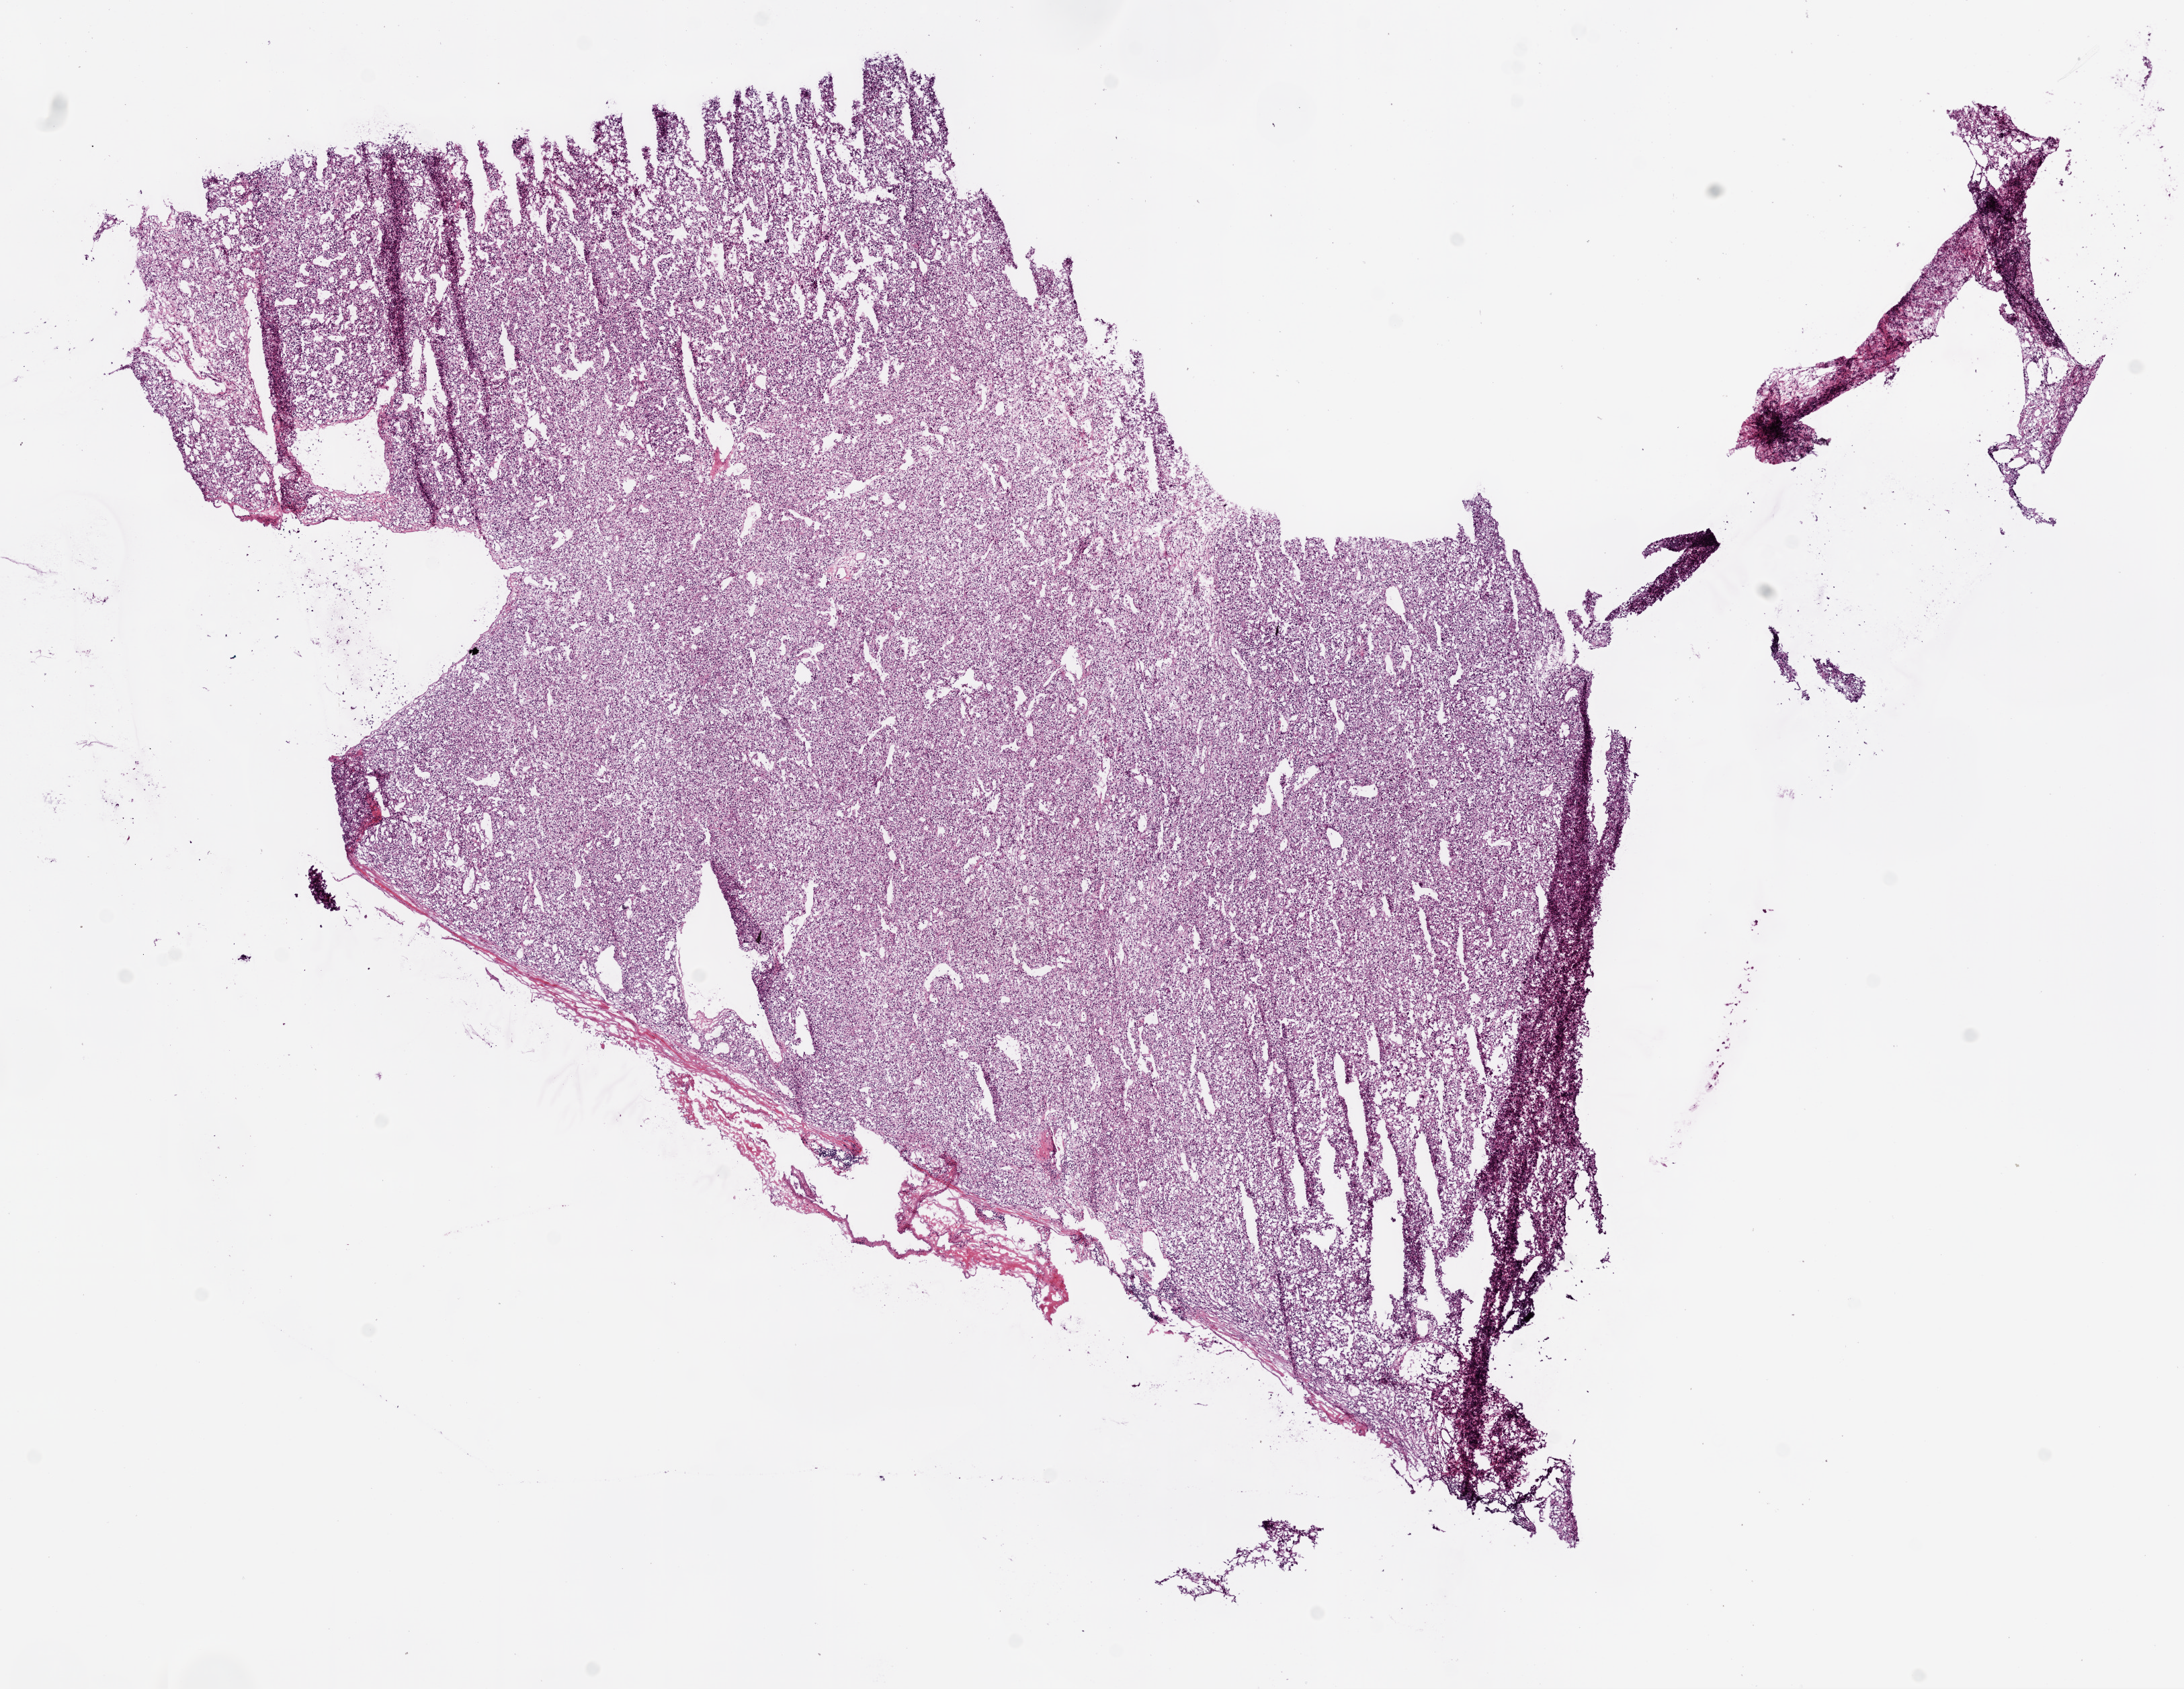
H&E-stained whole-slide image, whole scanned area (about 13.0 x 10.1 mm, slide scanned at 20x) shown as a low-resolution overview. Frozen section from the bottom of the tissue portion. Kidney, primary tumour sample. Male patient; age at initial diagnosis 79 years. Histologic grade: G3 (poorly differentiated). Composition of this section per pathologist review: tumour cells 95%, tumour nuclei 90%, normal cells 0%, stromal cells 5%, necrosis 0%.
- laterality: left
- AJCC pathologic stage: IV
- diagnosis: Clear cell adenocarcinoma, NOS